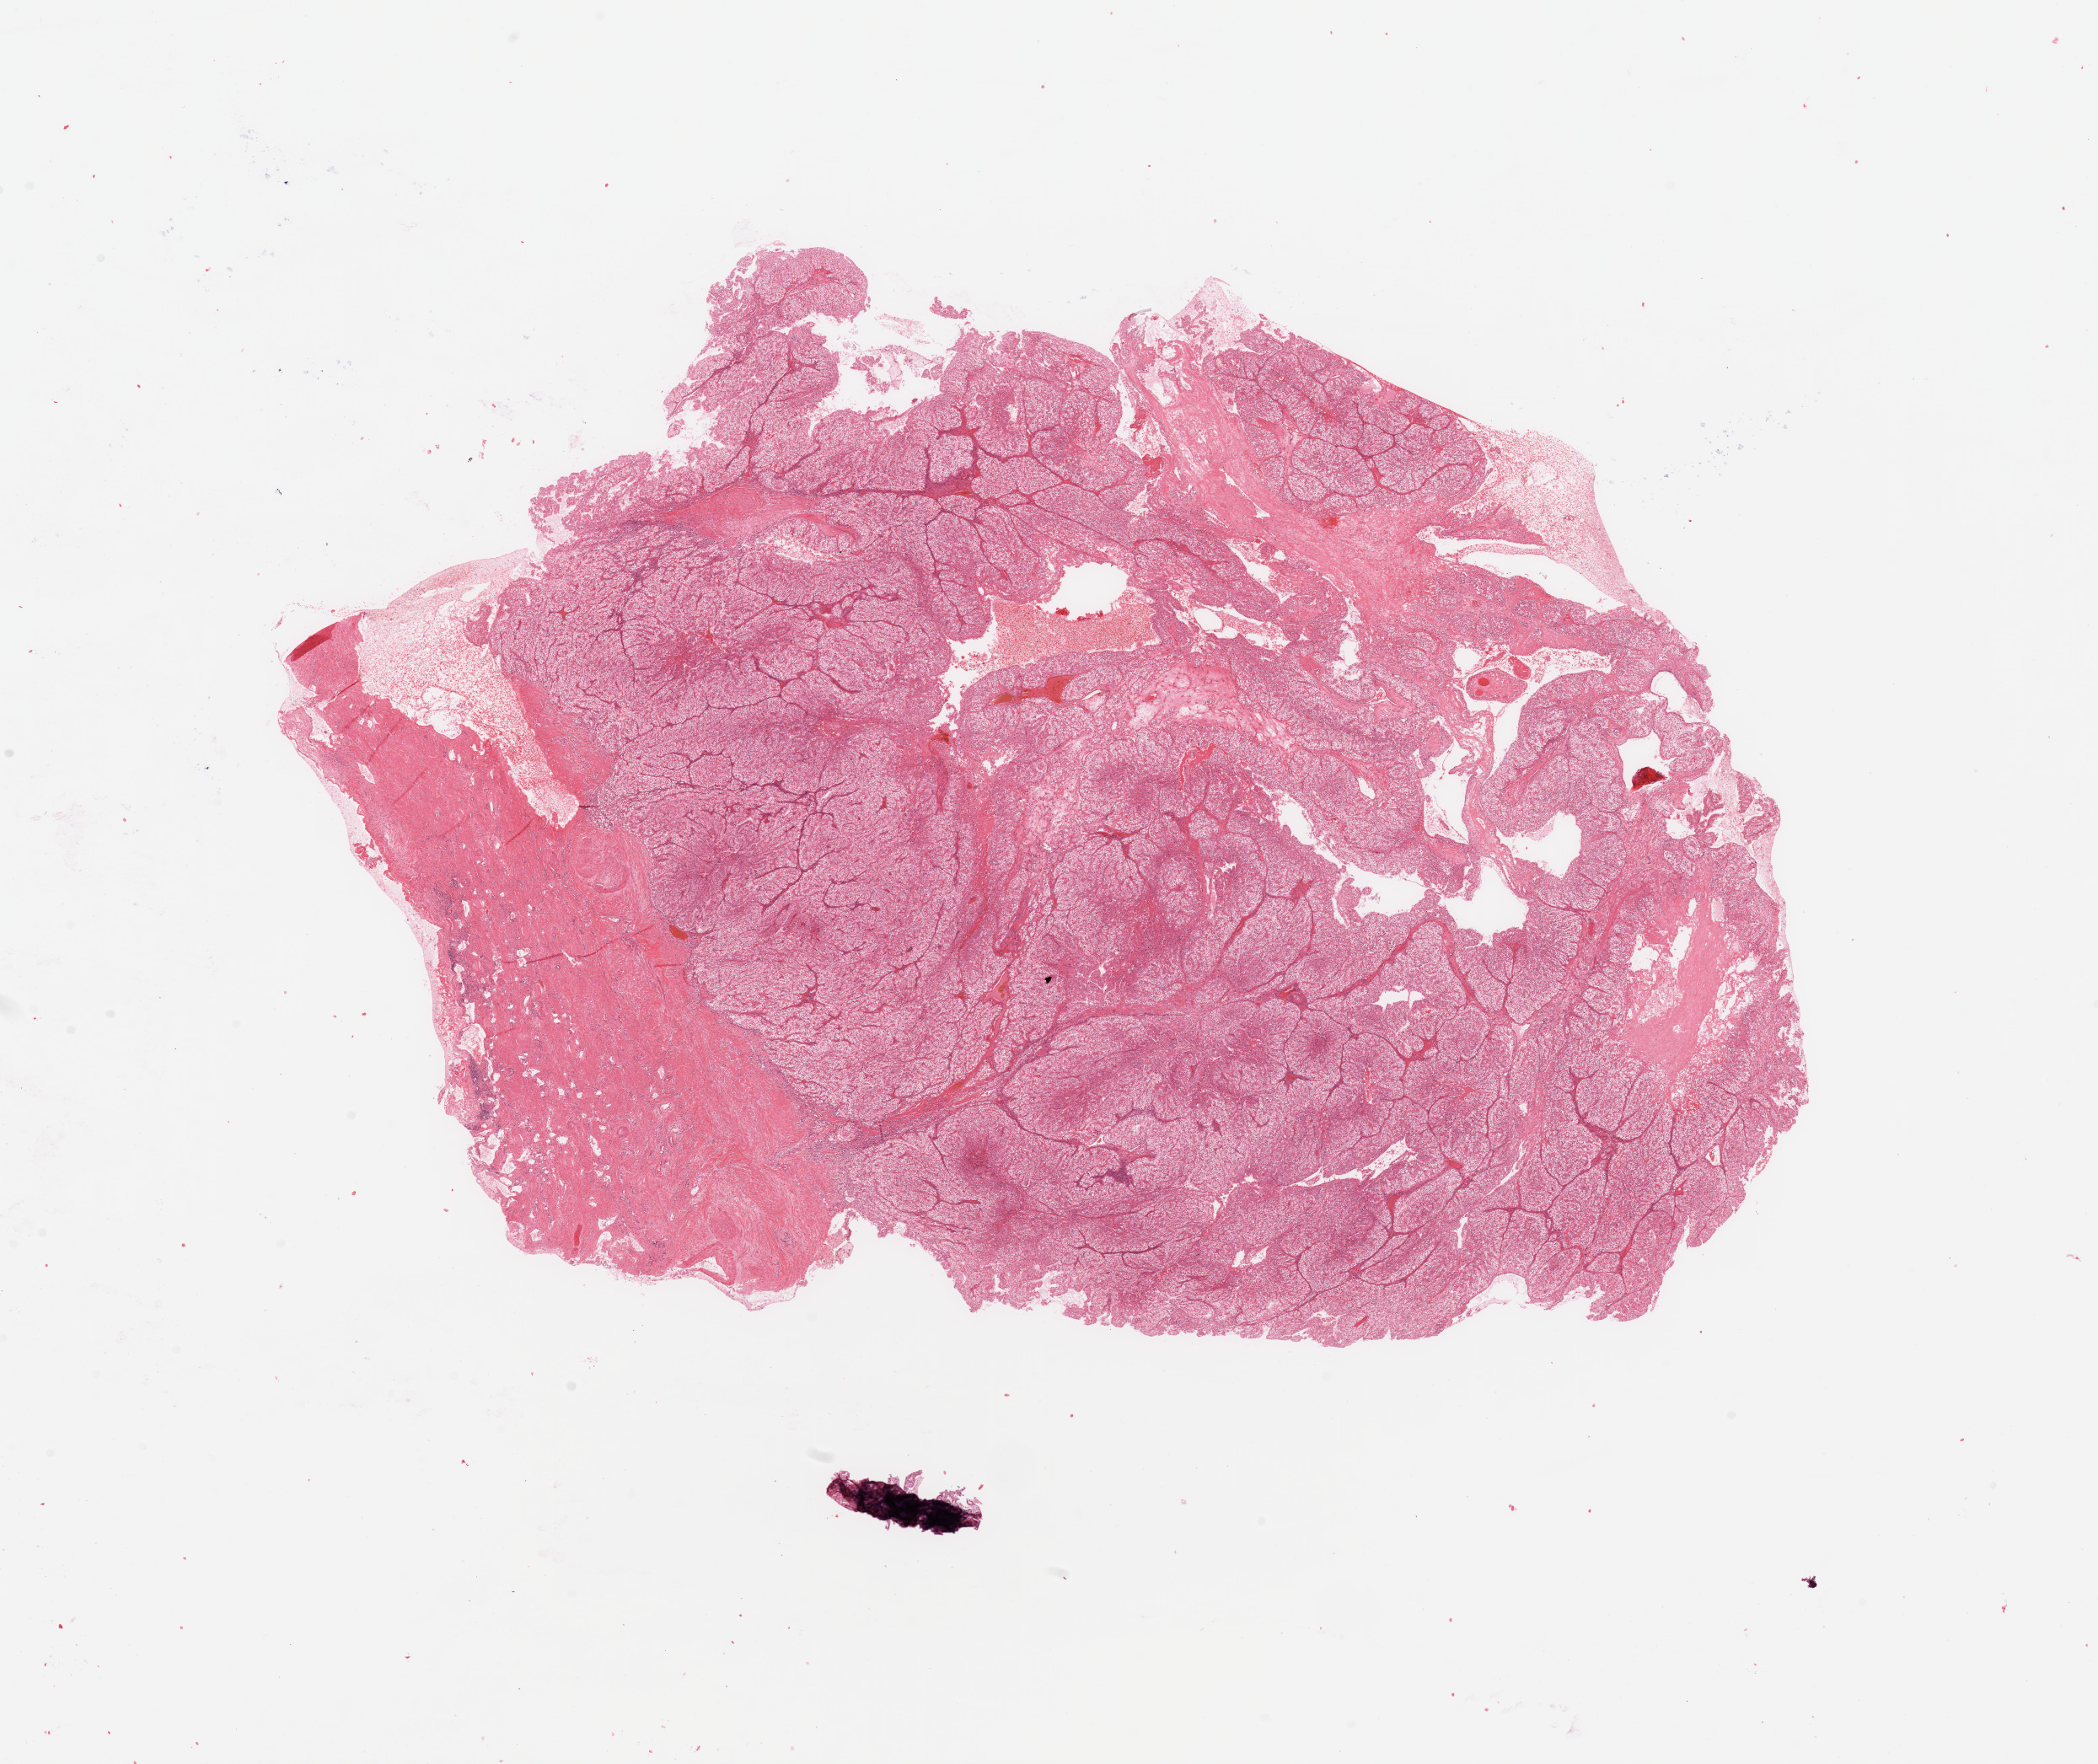
Hematoxylin and eosin (H&E) stained whole-slide image — low-resolution overview of the scanned area, about 19.7 x 16.6 mm (slide scanned at 20x). Tumour tissue sample, sampled site: kidney. Patient: male, age 61 years. Histologic grade: G2 (moderately differentiated). Pathologist review of this section (percent, as recorded): tumour nuclei 80%, necrosis 5%.
* AJCC pathologic stage: II
* diagnosis: Renal cell carcinoma, NOS